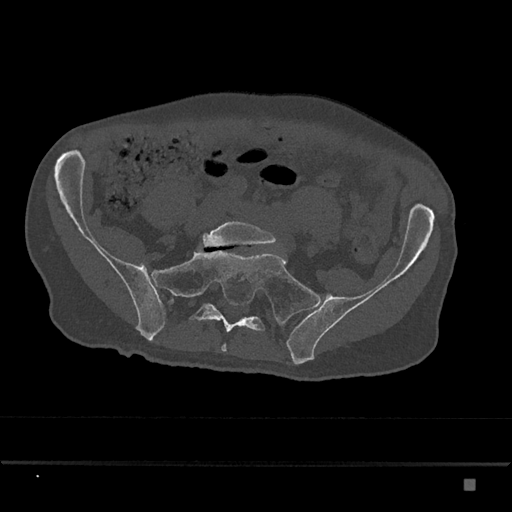
CT including the spine, one axial slice; position 223 of 797 along the scan axis; bone window (W 1800 / L 400 HU); 512 × 512 image matrix. Patient: male, 72 years. From the clinical record (not read from this slice): primary cancer: prostate.
Outlined on this slice (semi-automatically segmented with operator editing):
- L5 vertebra: box from (x=203, y=221) to (x=276, y=247) px